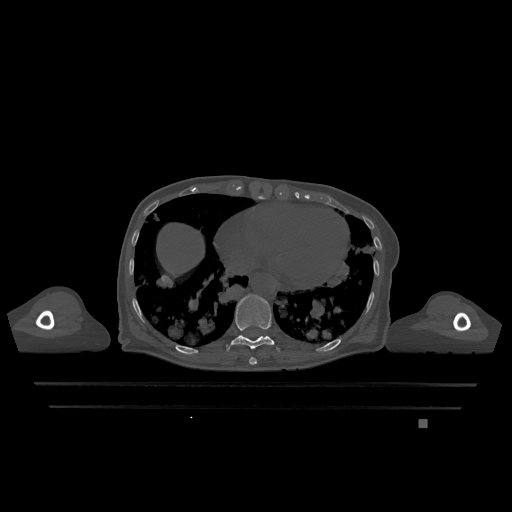
CT including the spine, one axial slice. Slice 641 of 1317 in the series (ordered by position). Bone window (W 1800 / L 400 HU). 0.5 mm slice thickness. 512 × 512 image matrix, field of view 500 × 500 mm. Female patient, age 74 years. Case-level facts recorded for this patient, not image findings: primary cancer: lung.
Annotated regions visible in this slice (semi-automatic segmentation, software-assisted and operator-edited):
- T10 vertebra: box from (x=226, y=294) to (x=280, y=352) px
- T9 vertebra: (x=249, y=357)–(x=257, y=365)